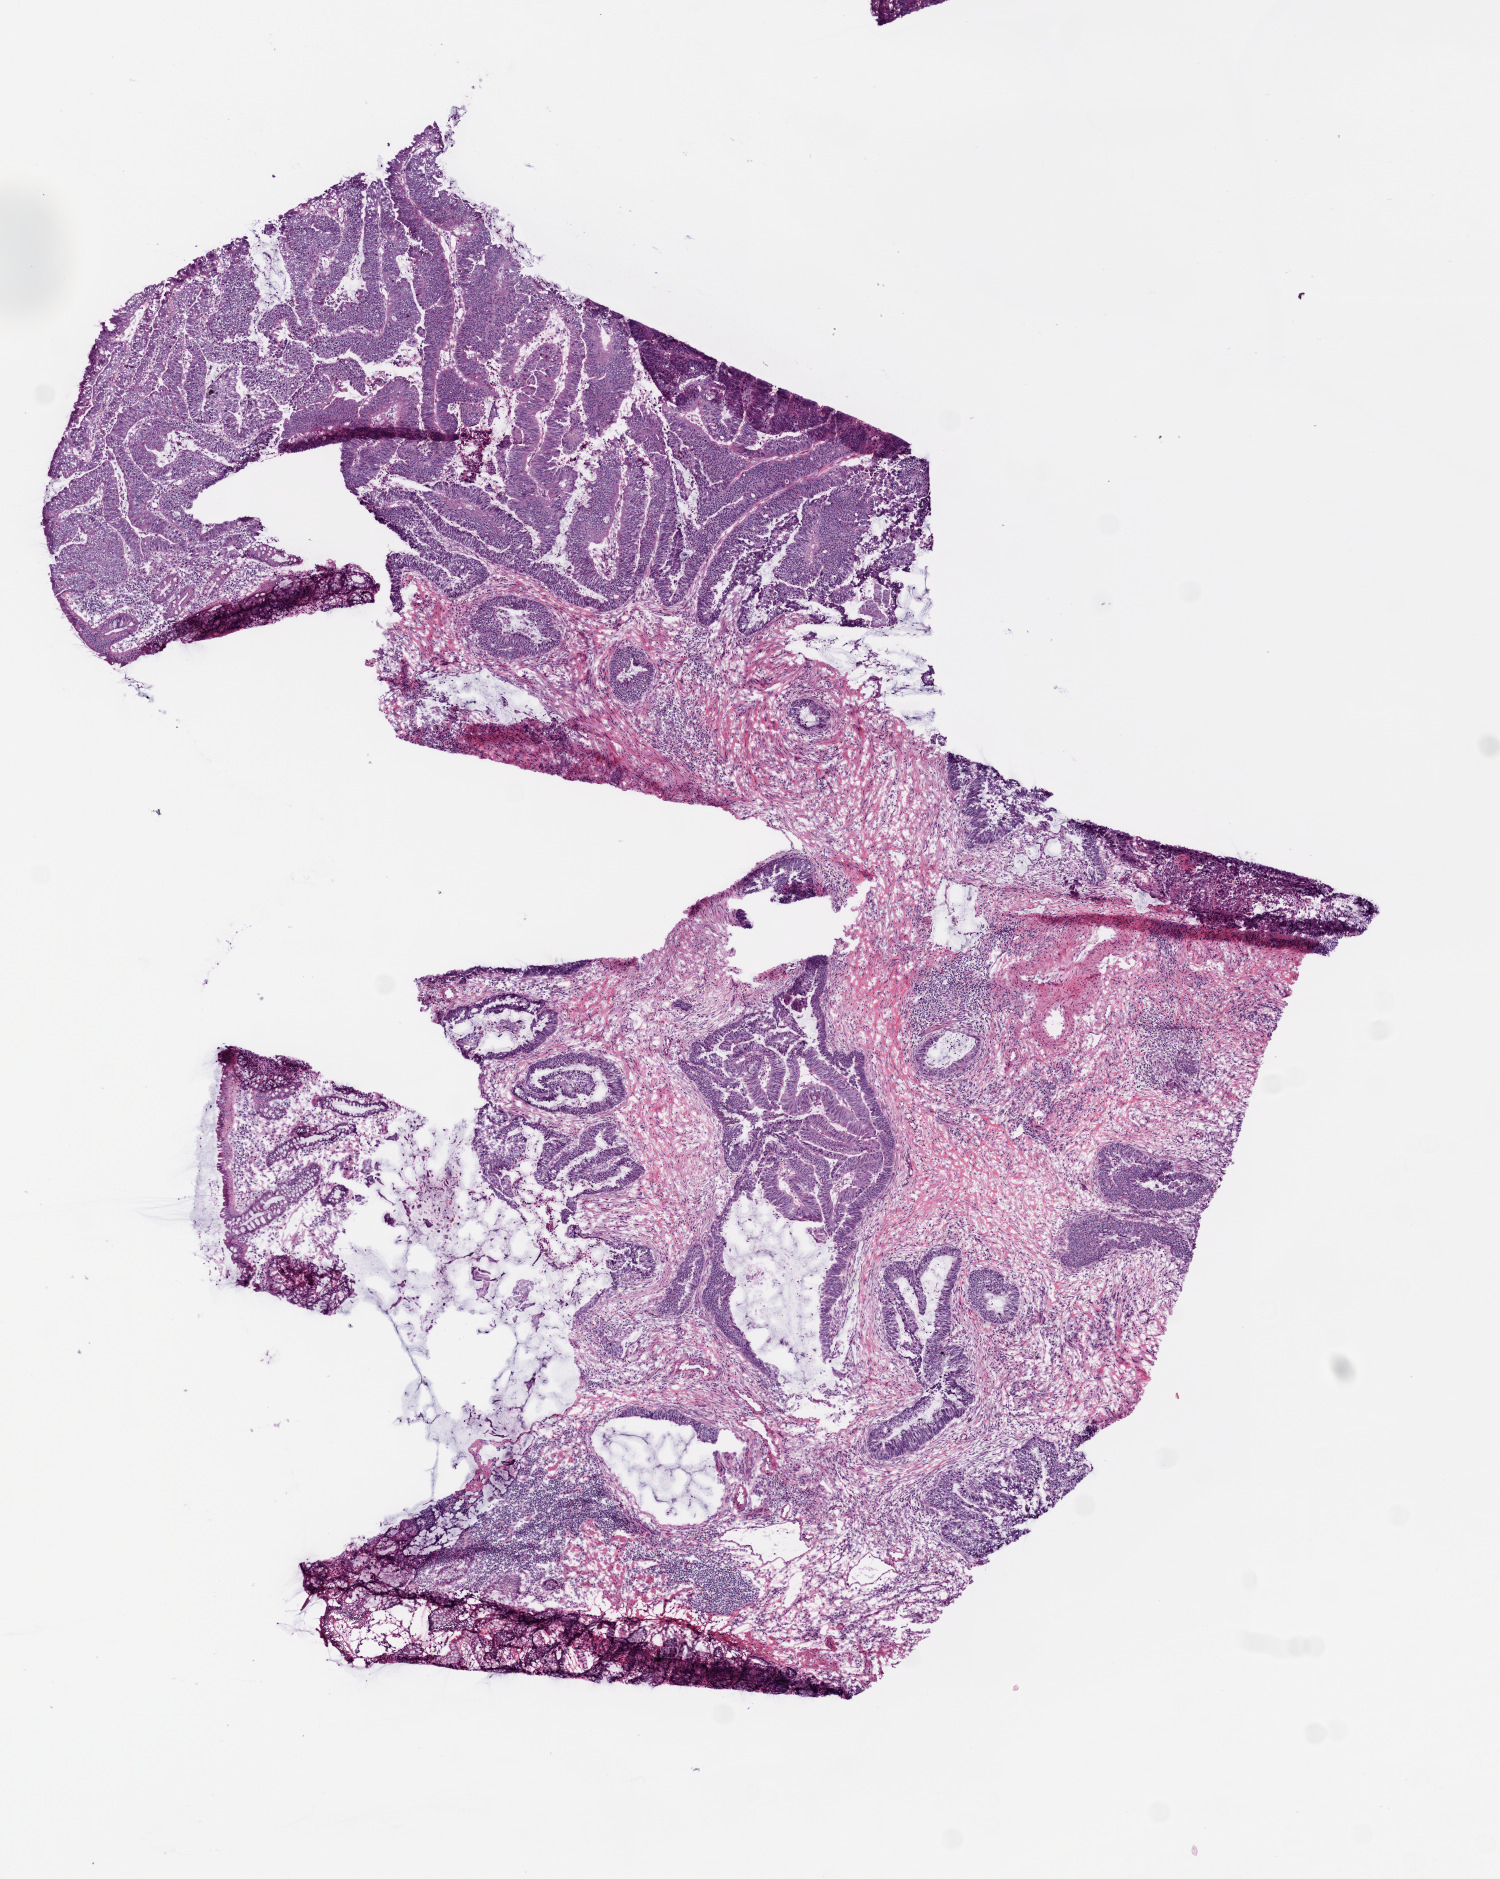
Whole-slide histology image, H&E, a low-resolution overview of the entire scanned area, about 6.0 x 7.5 mm, frozen section from the bottom of the tissue portion, colon, primary tumour sample. Male, age 78 years at initial diagnosis. Composition of this section per pathologist review: tumour cells 40%, tumour nuclei 60%, normal cells 0%, stromal cells 60%, necrosis 0%.
Lymph nodes positive (case pathology): 0 of 22 examined. Diagnosis: Mucinous adenocarcinoma (sigmoid colon). AJCC pathologic stage: I (6th edition).